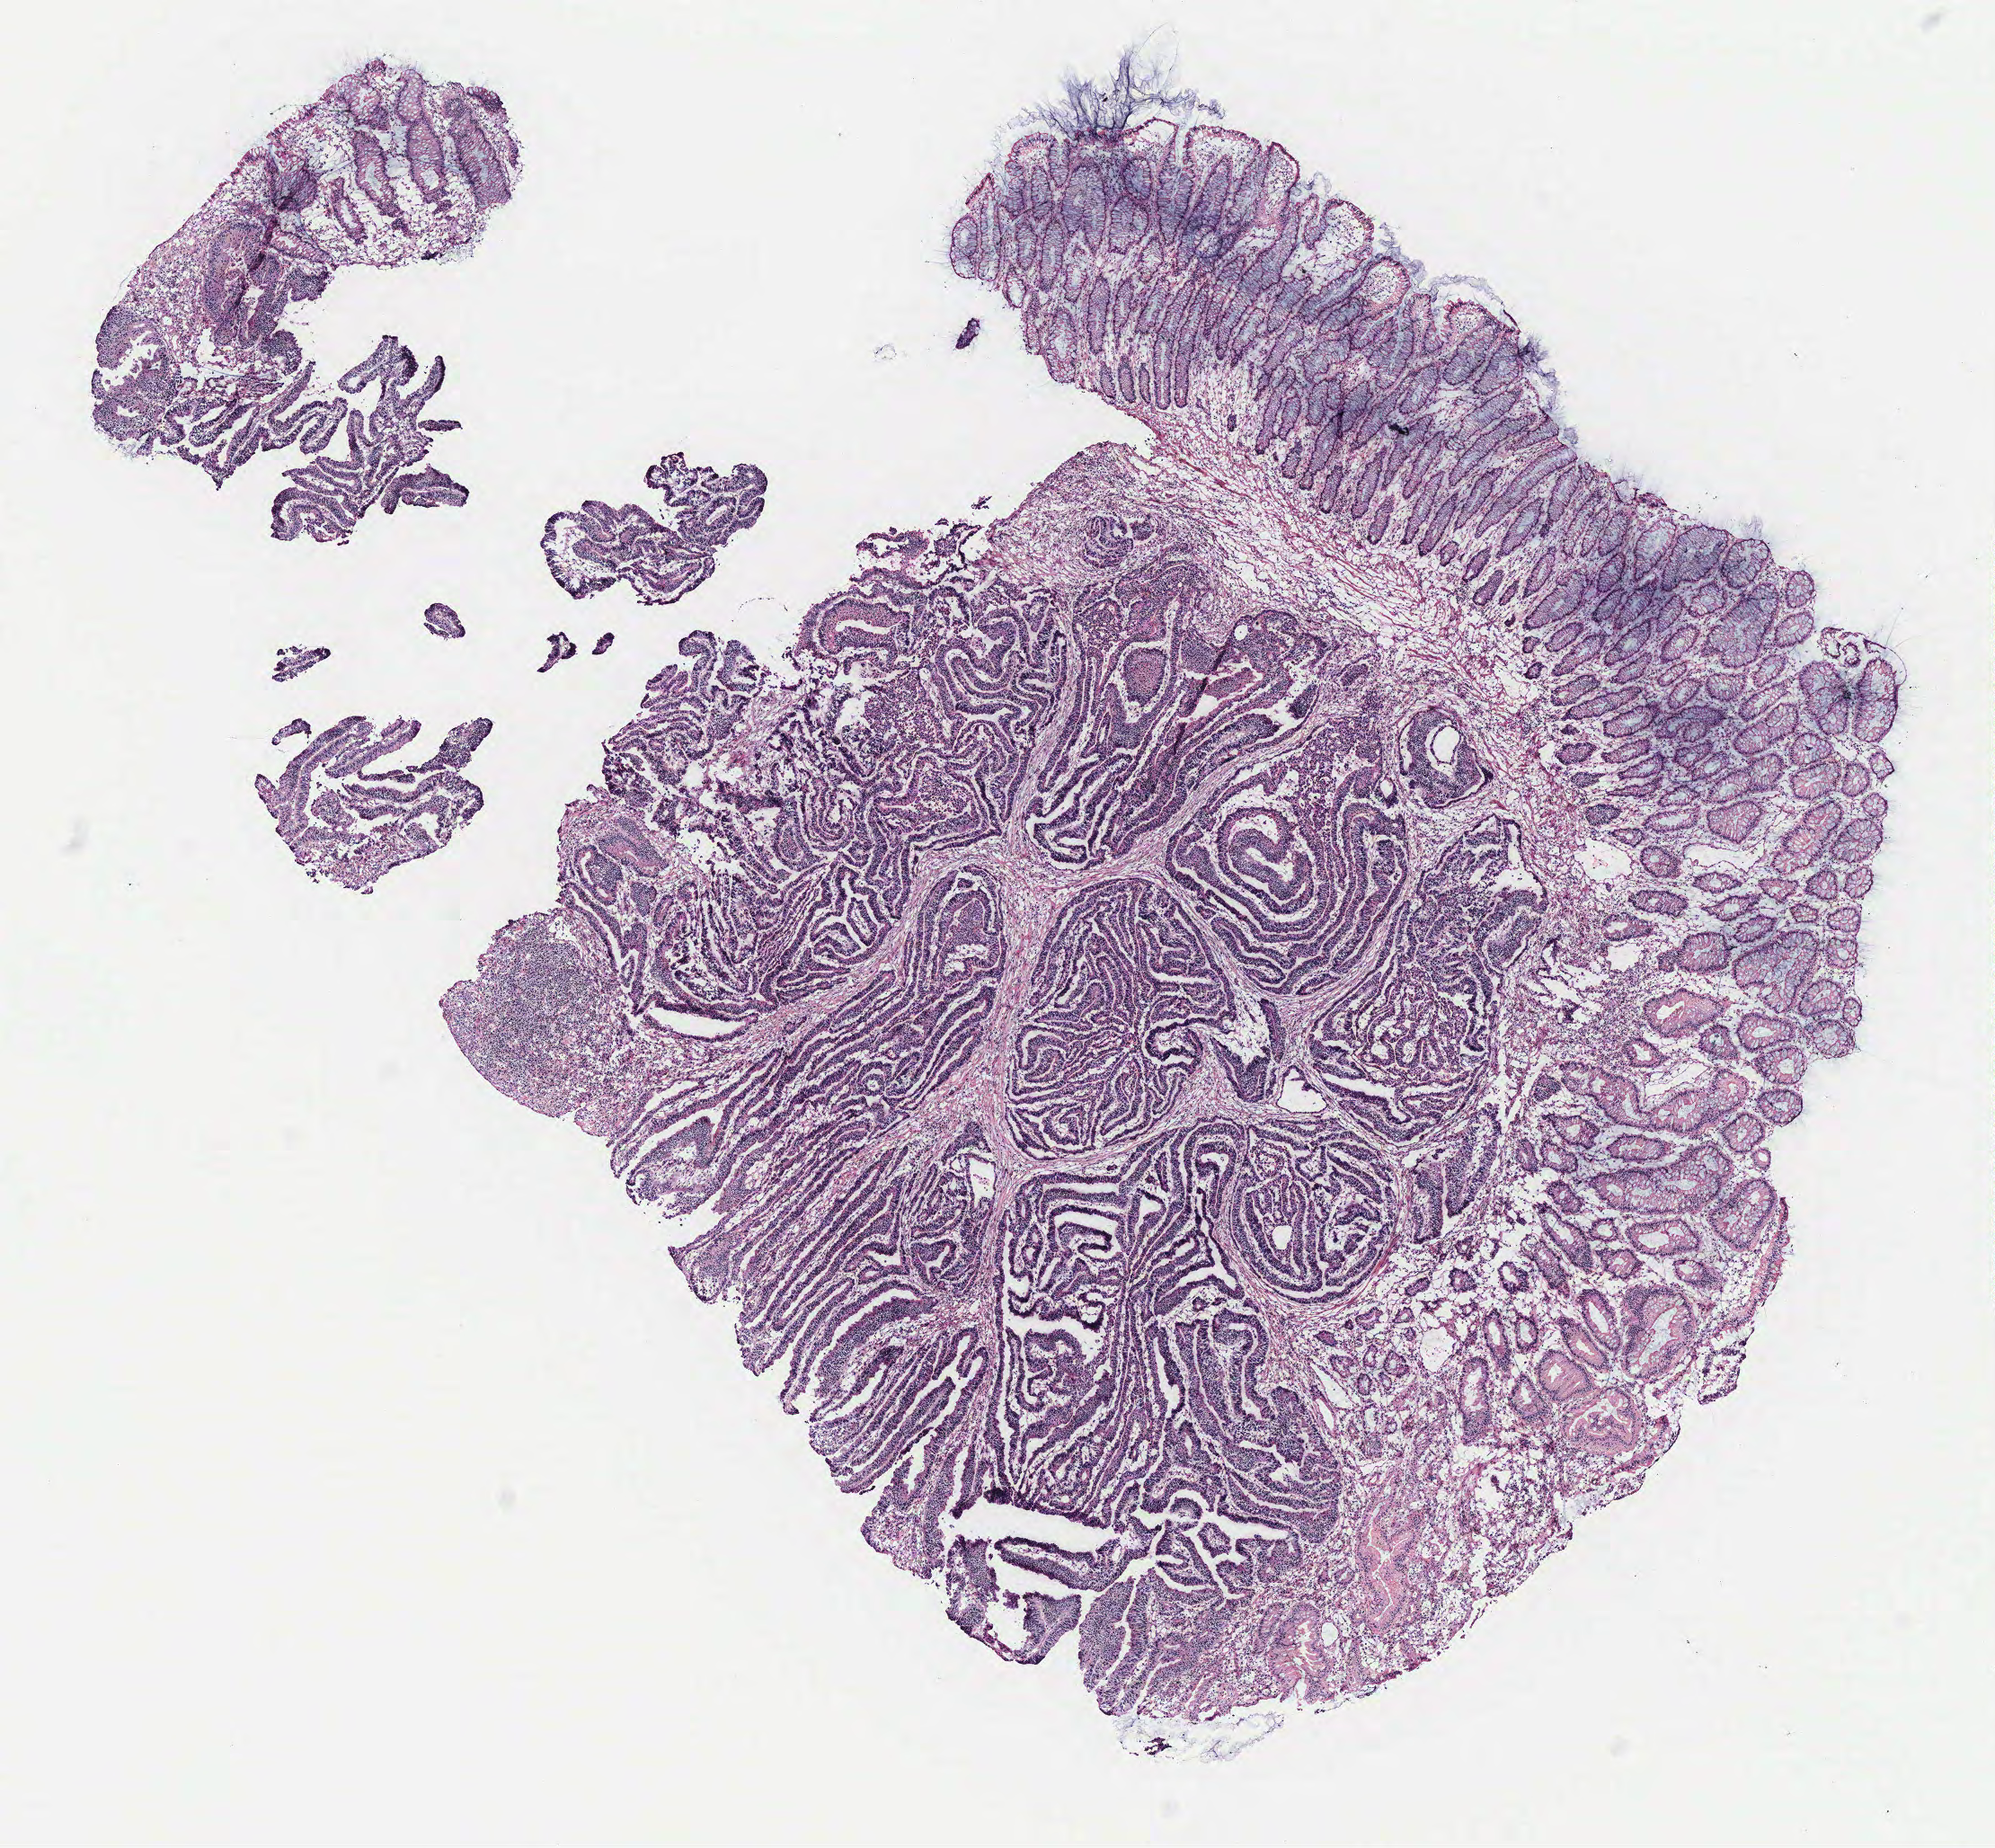
Whole-slide histology image, H&E-stained, a low-resolution overview of the entire scanned area, about 8.9 x 8.2 mm; colon, tissue type not recorded.
Patient diagnosis (cohort enrolment): colon cancer (colon).